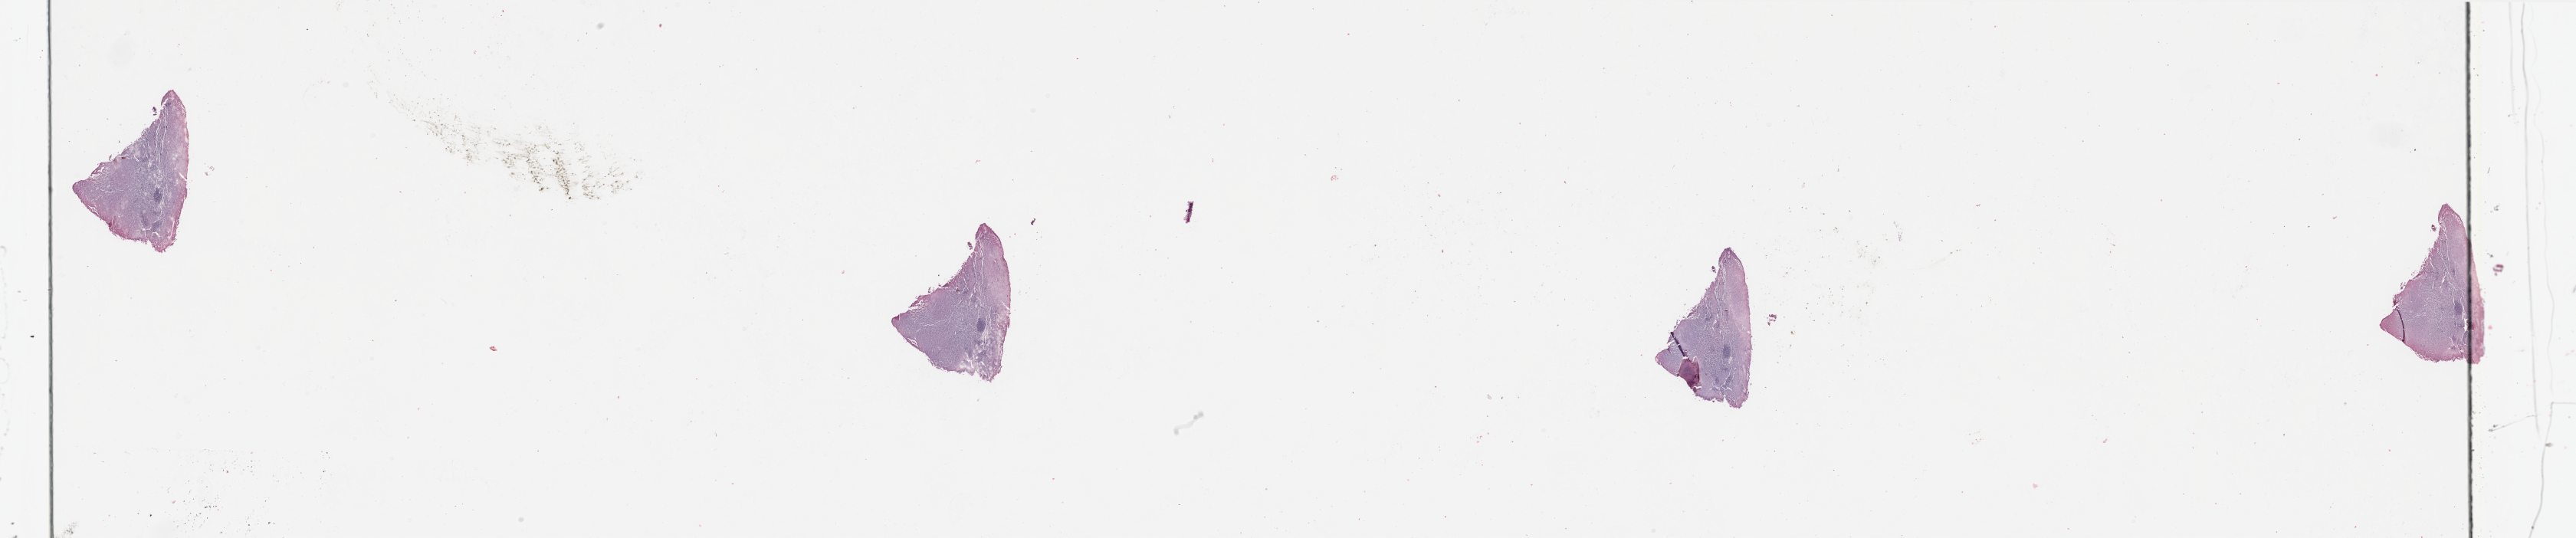
Whole-slide histology image, H&E-stained, whole scanned area (about 53.2 x 11.1 mm, from a 20x scan) shown as a low-resolution overview. Tumour tissue sample, sampled site: lymph node. Patient: male, age 56 years. Composition of this section per pathologist review: tumour nuclei 98%, necrosis 2%.
This section: metastatic tumour tissue. Patient diagnosis: Malignant melanoma, NOS.